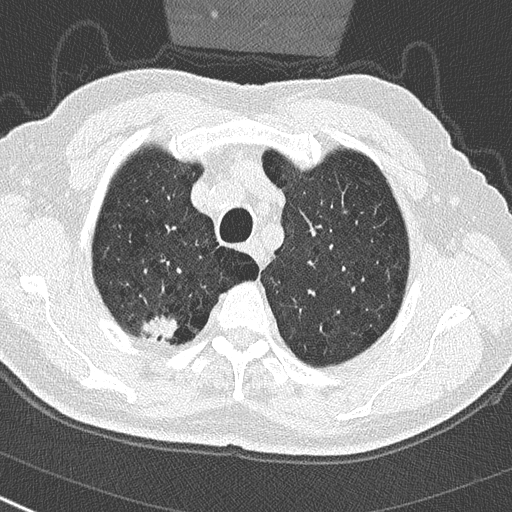
Low-dose screening chest CT, one axial slice; position 240 of 290 along the scan axis; 120 kVp; lung window (W 1500 / L -600 HU); 2 mm slice thickness; 512 × 512 image matrix, field of view 300 × 300 mm.
Annotated regions visible in this slice (manually delineated by an expert):
- lesion 1 (tumor, upper lobe of right lung): bounding box <140,316,178,343> (left, top, right, bottom; pixels)